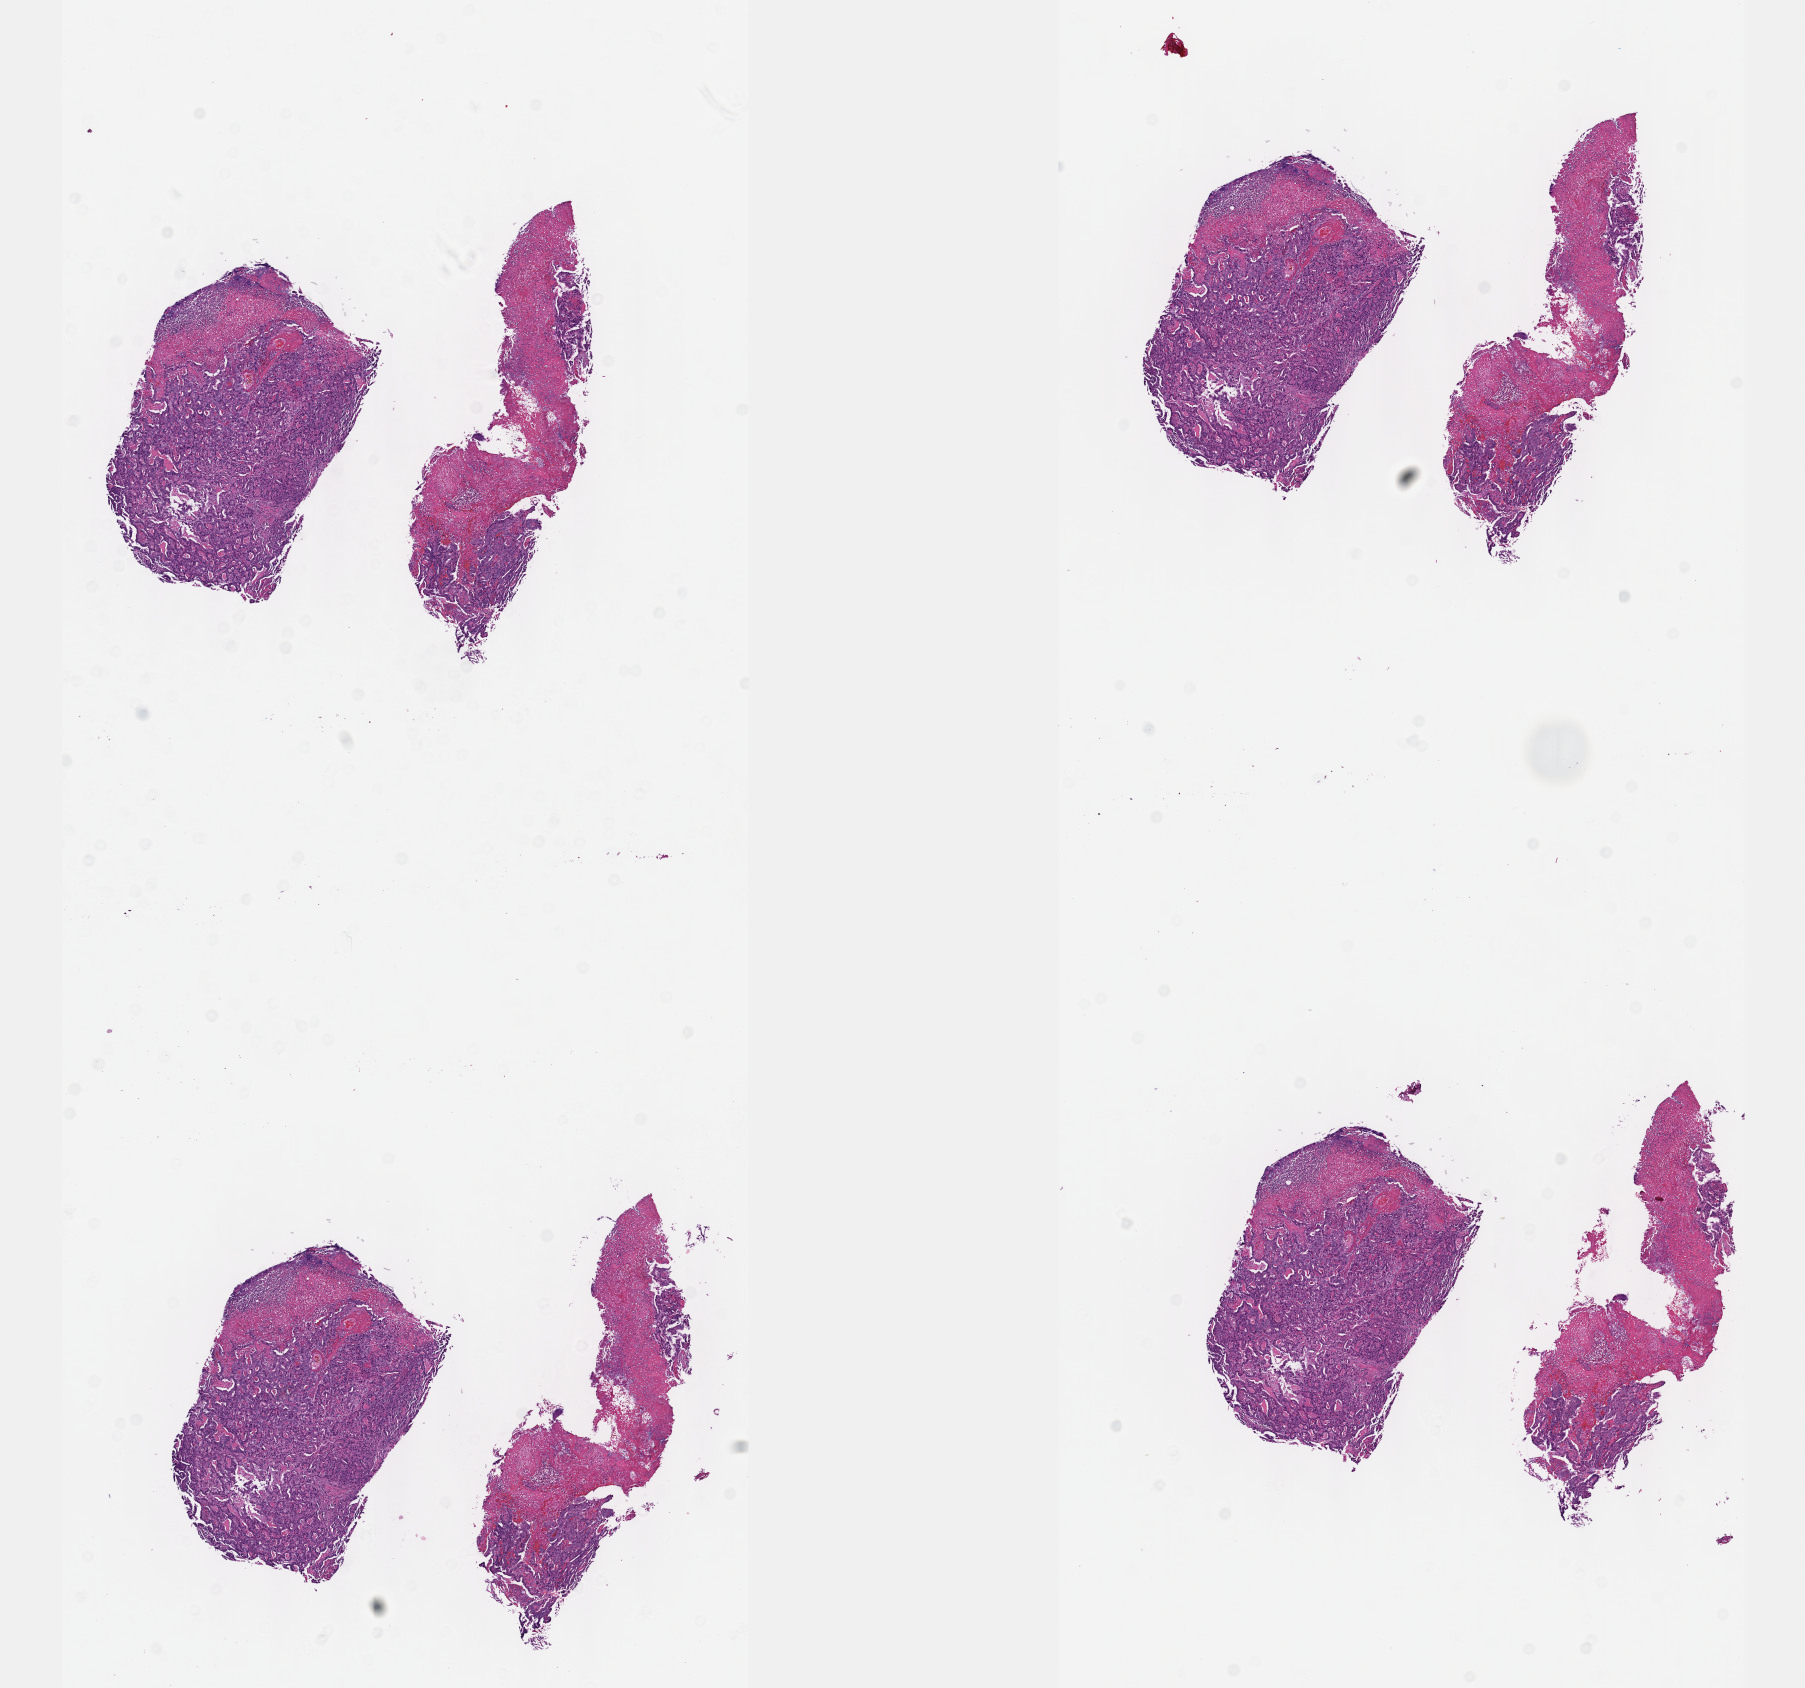
Whole-slide histology image, H&E-stained — low-resolution overview of the scanned area, about 14.6 x 13.6 mm; formalin-fixed paraffin-embedded (FFPE) diagnostic section; sample: primary tumour, esophagus. Male, age 72 years at initial diagnosis. Histologic grade: G3 (poorly differentiated).
Pathologic diagnosis: Adenocarcinoma, NOS.